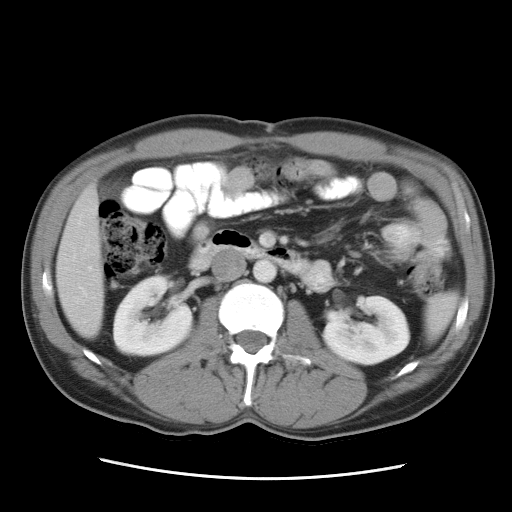
Contrast-enhanced abdominal CT, one axial slice; position 10 of 34 along the scan axis; reconstruction kernel STANDARD; intravenous contrast given; soft-tissue window (W 400 / L 40 HU); 512 × 512 image matrix. Male patient, age 40 years. Case-level facts recorded for this patient, not image findings: diagnosis: colorectal cancer liver metastases, imaged before liver resection; multiple liver metastases: yes; largest metastasis: 1.5 cm; chemotherapy before resection: no.
Outlined on this slice (expert manual segmentation):
- liver: bounding box <58,185,105,334> (left, top, right, bottom; pixels)
- planned liver remnant (the part of the liver to remain after resection): <61,185,102,334>
- portal vein (with intrahepatic branches): <89,268,91,270>